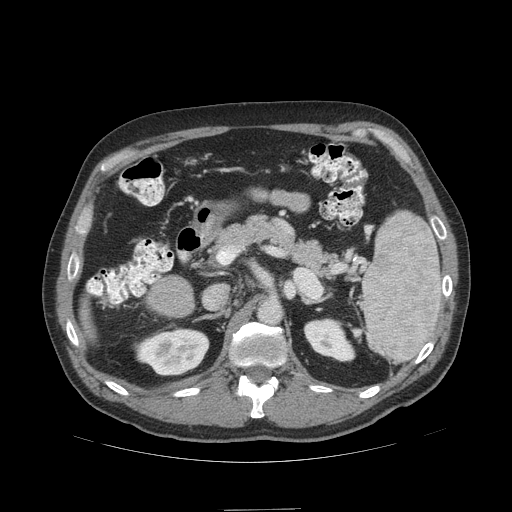
Contrast-enhanced abdominal CT (liver protocol), one axial slice. Reconstruction kernel STANDARD. 140 kVp. Soft-tissue window (W 400 / L 40 HU). 2.5 mm slice thickness. 512 × 512 image matrix, field of view 440 × 440 mm. Case-level facts recorded for this patient, not image findings: diagnosis: hepatocellular carcinoma (patient treated with transarterial chemoembolisation; whether this scan precedes or follows treatment is not stated here); TNM stage (as recorded): Stage-I; Child-Pugh class: A; tumour differentiation: no biopsy; tumour nodularity: uninodular.
Structures marked on this image (semi-automatic segmentation, software-assisted and operator-edited):
- liver parenchyma outside the tumour (the mass and vessels are separate outlines, so this box may not span the whole liver): bounding box (x1, y1, x2, y2) in pixels: (80, 300, 96, 340)